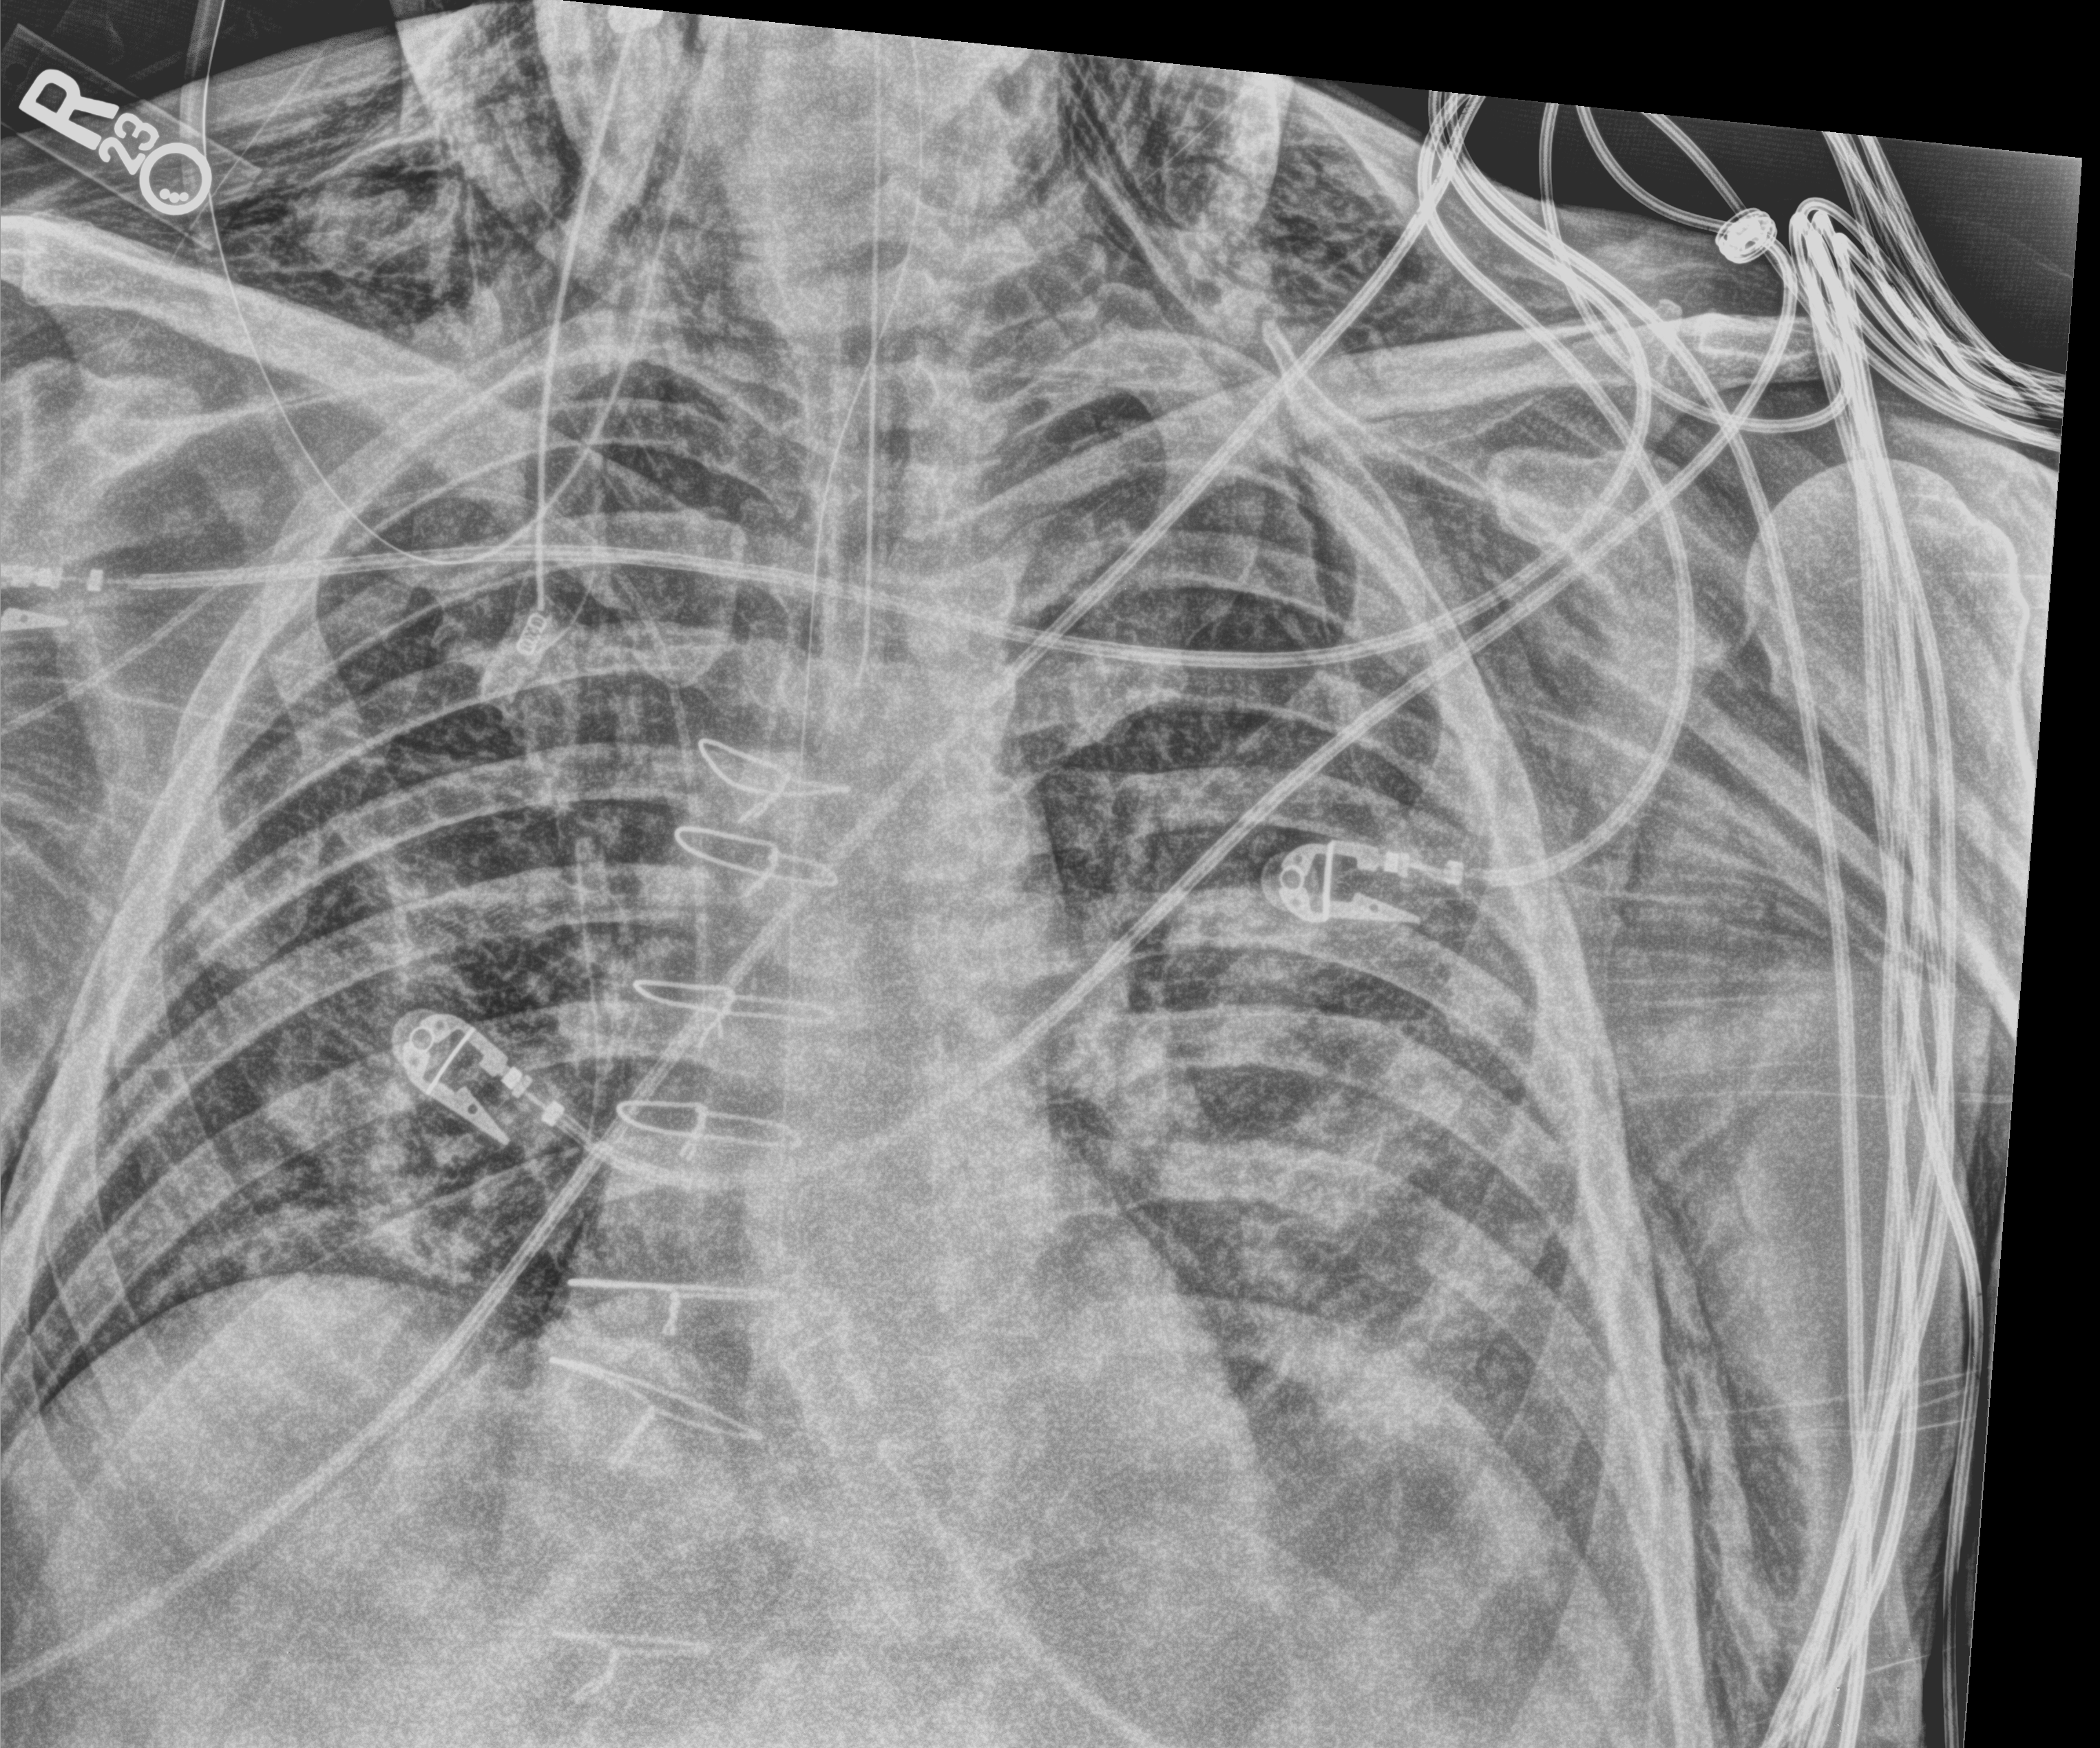
Chest X-ray (portable), anteroposterior (AP) projection. Male patient hospitalised with COVID-19, age 60–74 years.
Hospital-stay facts (about this admission, not read from this image; timing relative to this image not recorded): mechanically ventilated during this hospital stay: yes.